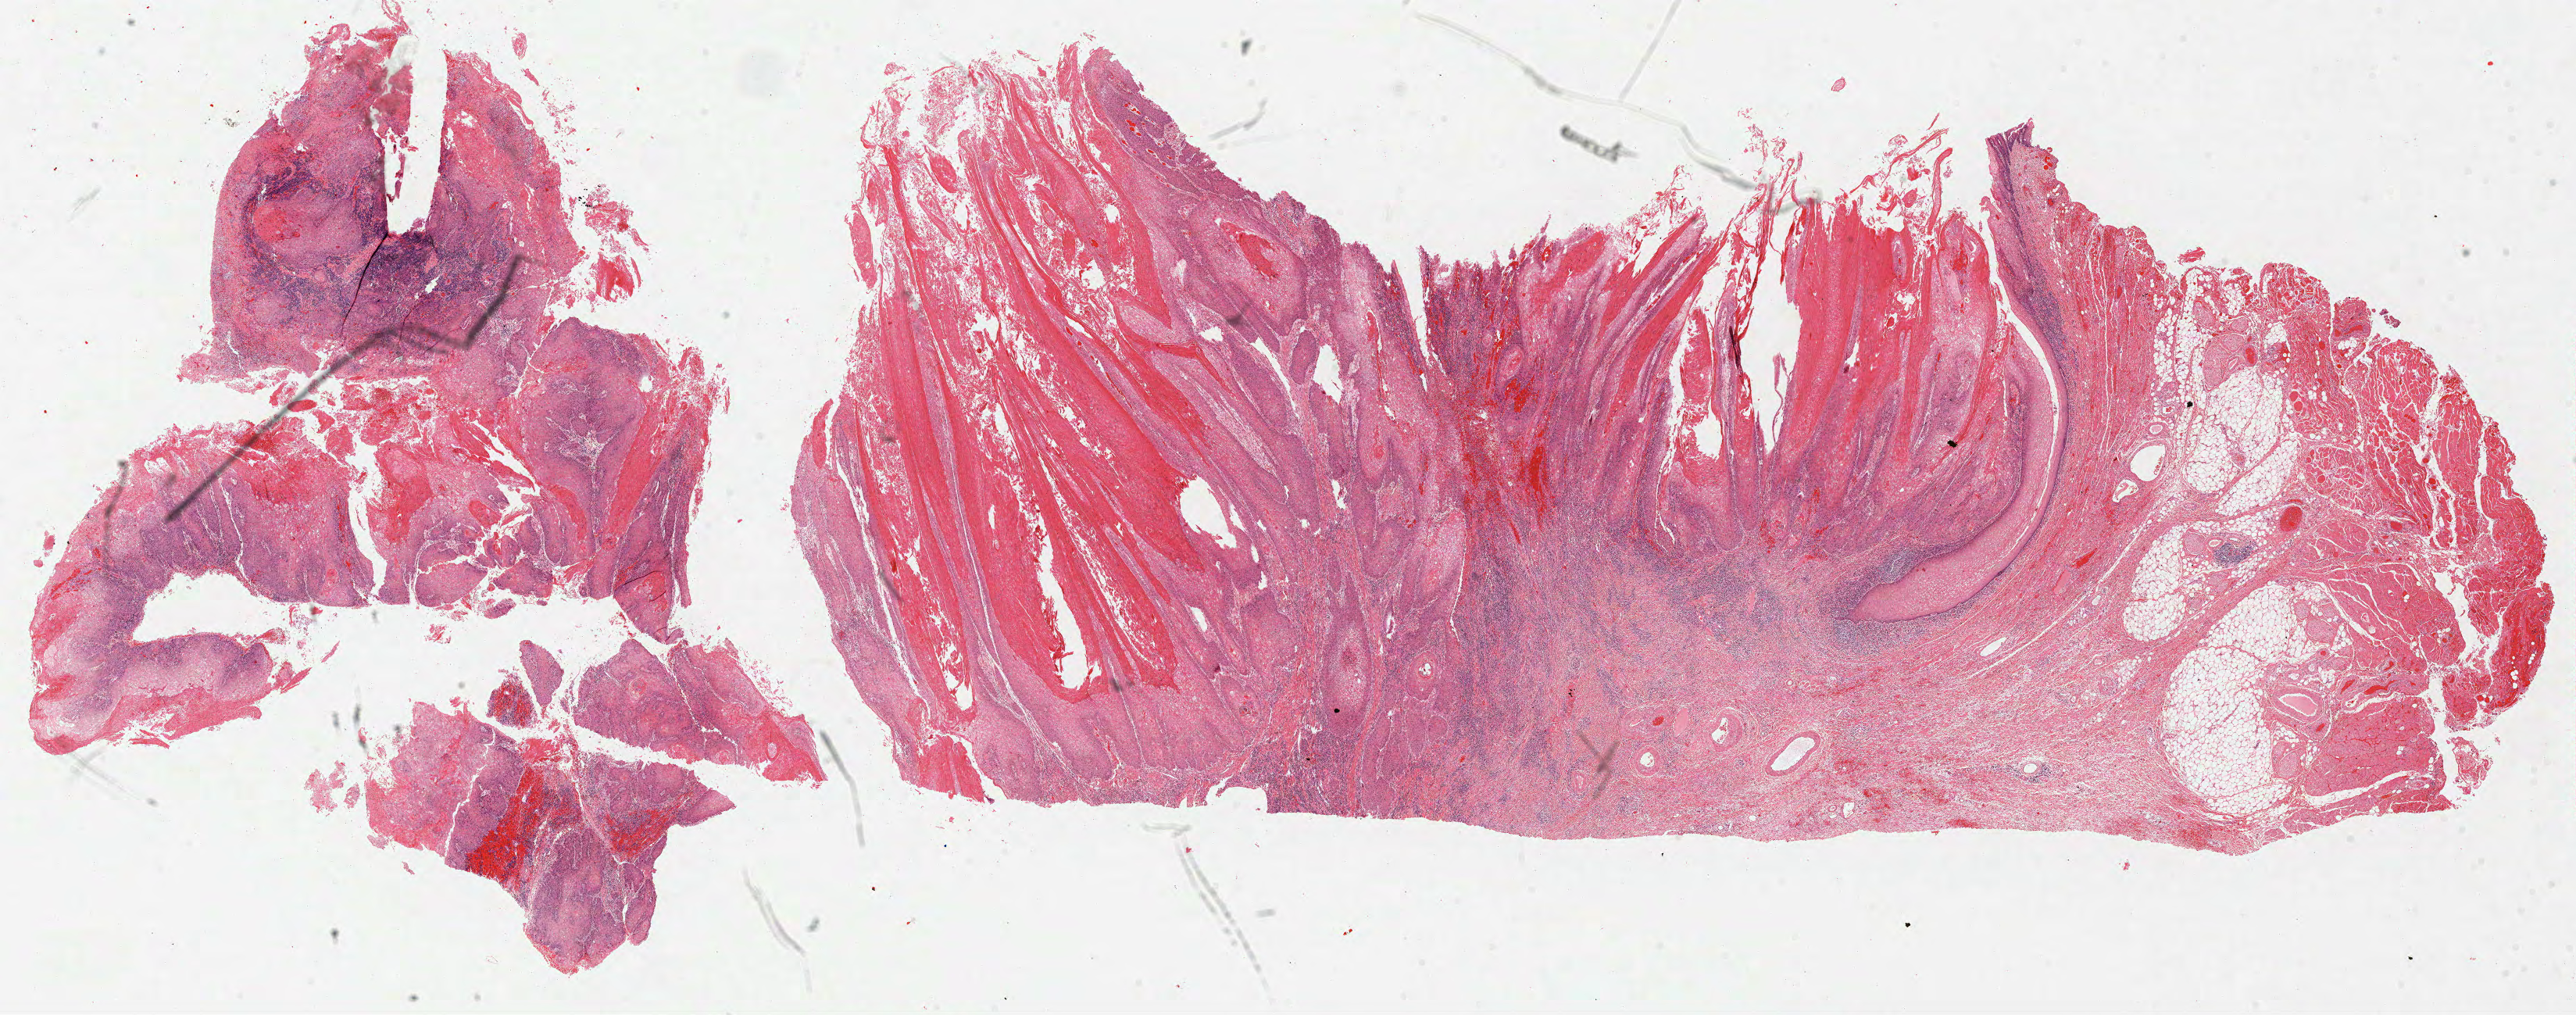
Digitized Hematoxylin and eosin (H&E) stained tissue section (whole slide) — low-resolution overview of the scanned area, about 26.6 x 10.5 mm, formalin-fixed paraffin-embedded (FFPE) diagnostic section, sample: primary tumour, head and neck. Female, age 68 years at initial diagnosis. Histologic grade: G1 (well differentiated).
* AJCC pathologic stage: IVA (7th edition)
* laterality: left
* pathologic diagnosis: Squamous cell carcinoma, NOS (overlapping lesion of lip, oral cavity and pharynx)